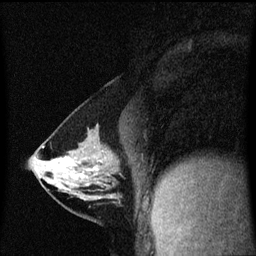
Breast MRI (dynamic contrast-enhanced), one sagittal slice; position 28 of 60 along the scan axis; dynamic contrast-enhanced series, image 2 of 3 at this slice position (ordered by acquisition); 1.5 T; TE 4.2 ms, TR 8.4 ms; 2 mm slice thickness; 256 × 256 image matrix, field of view 200 × 200 mm. Female patient, age 40 years. Case-level facts recorded for this patient, not image findings: setting: breast cancer imaged before/during neoadjuvant chemotherapy; receptor status: triple-negative.
Structures marked on this image (semi-automatically segmented with operator editing):
- analysis volume of interest (the breast-tissue region the enhancement analysis was run in; not a lesion): box from (x=34, y=142) to (x=122, y=199) px
- tumour enhancement mask (voxels above the 70 % enhancement threshold inside the analysis volume of interest): (x=65, y=156)–(x=98, y=177)